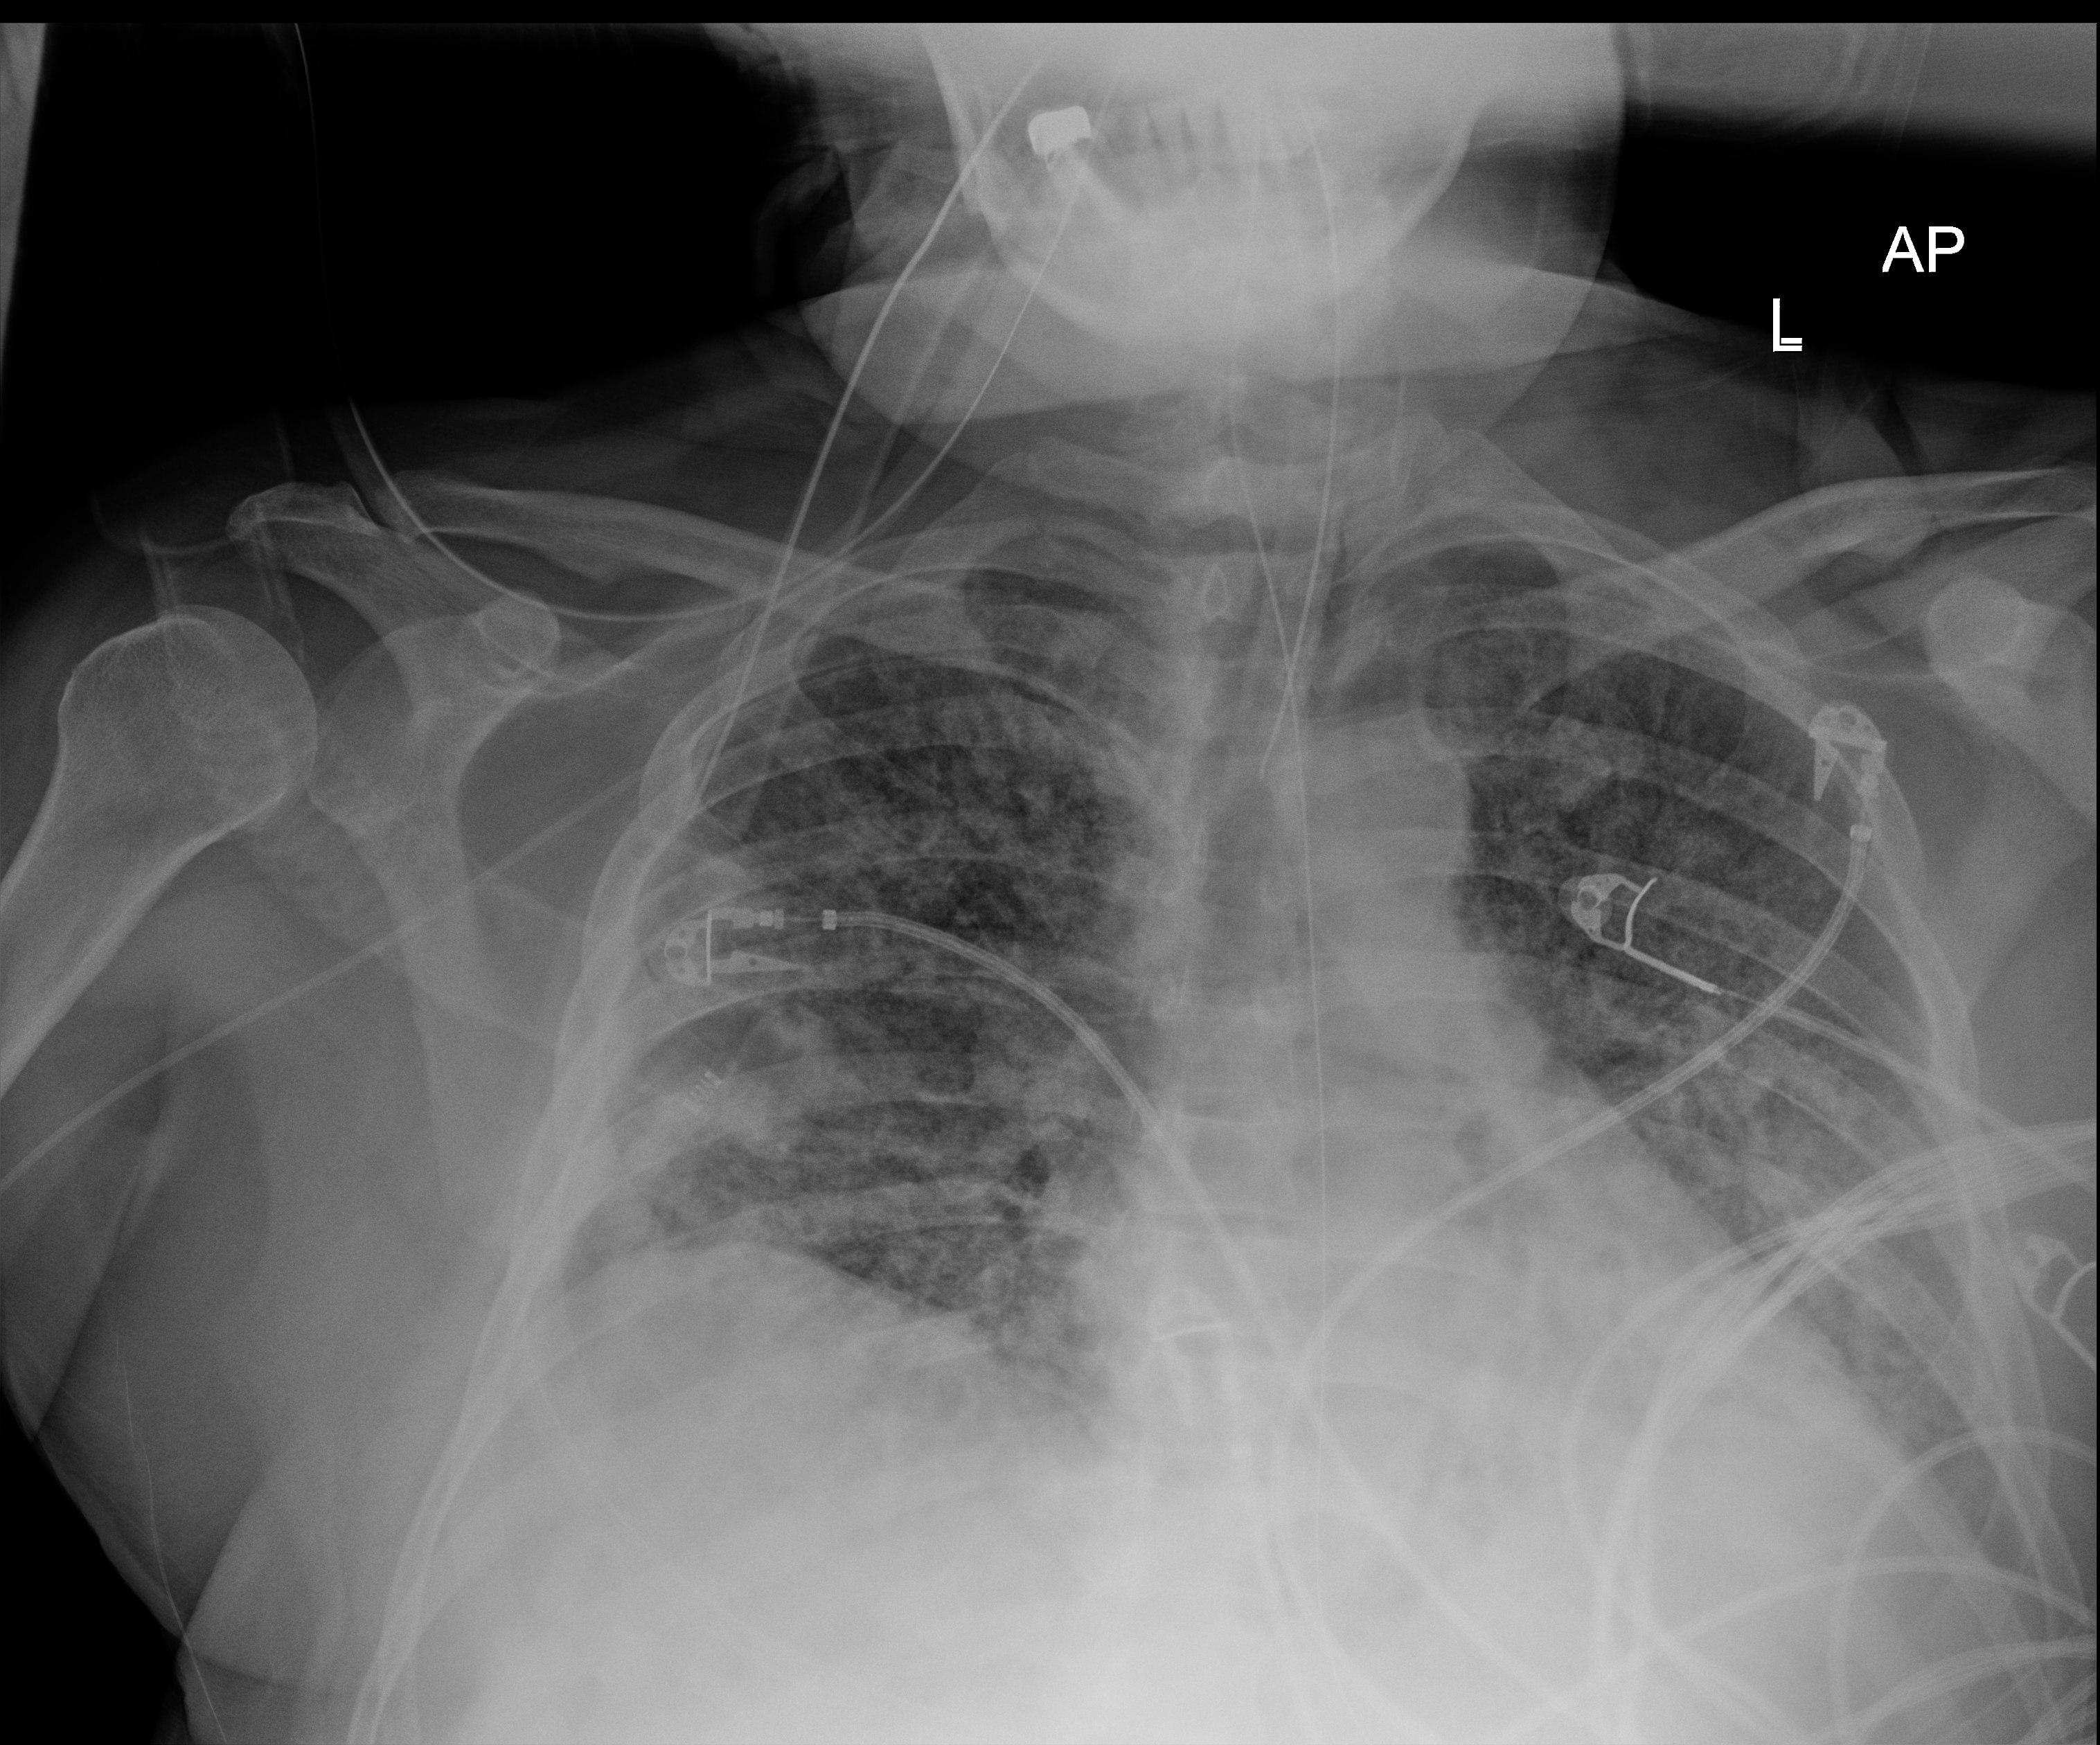
Bedside chest radiograph (digital radiography); anteroposterior (AP) projection. Male patient hospitalised with COVID-19, age 18–59 years.
Hospital-stay facts (about this admission, not read from this image; timing relative to this image not recorded):
- diabetes (admission record): no
- admitted to intensive care during this hospital stay: yes
- length of hospital stay: 96 days